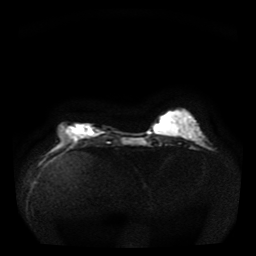
Breast MRI, one axial slice. Position 11 of 36 along the scan axis. Diffusion-weighted series; image 2 of 4 stored at this slice position (different b-values; order by instance number). 1.5 T. 256 × 256 image matrix, field of view 330 × 330 mm. Female patient.
Outlined on this slice (outlined manually by an expert reader):
- tumour on diffusion-weighted imaging: bounding box <72,125,96,135> (left, top, right, bottom; pixels)